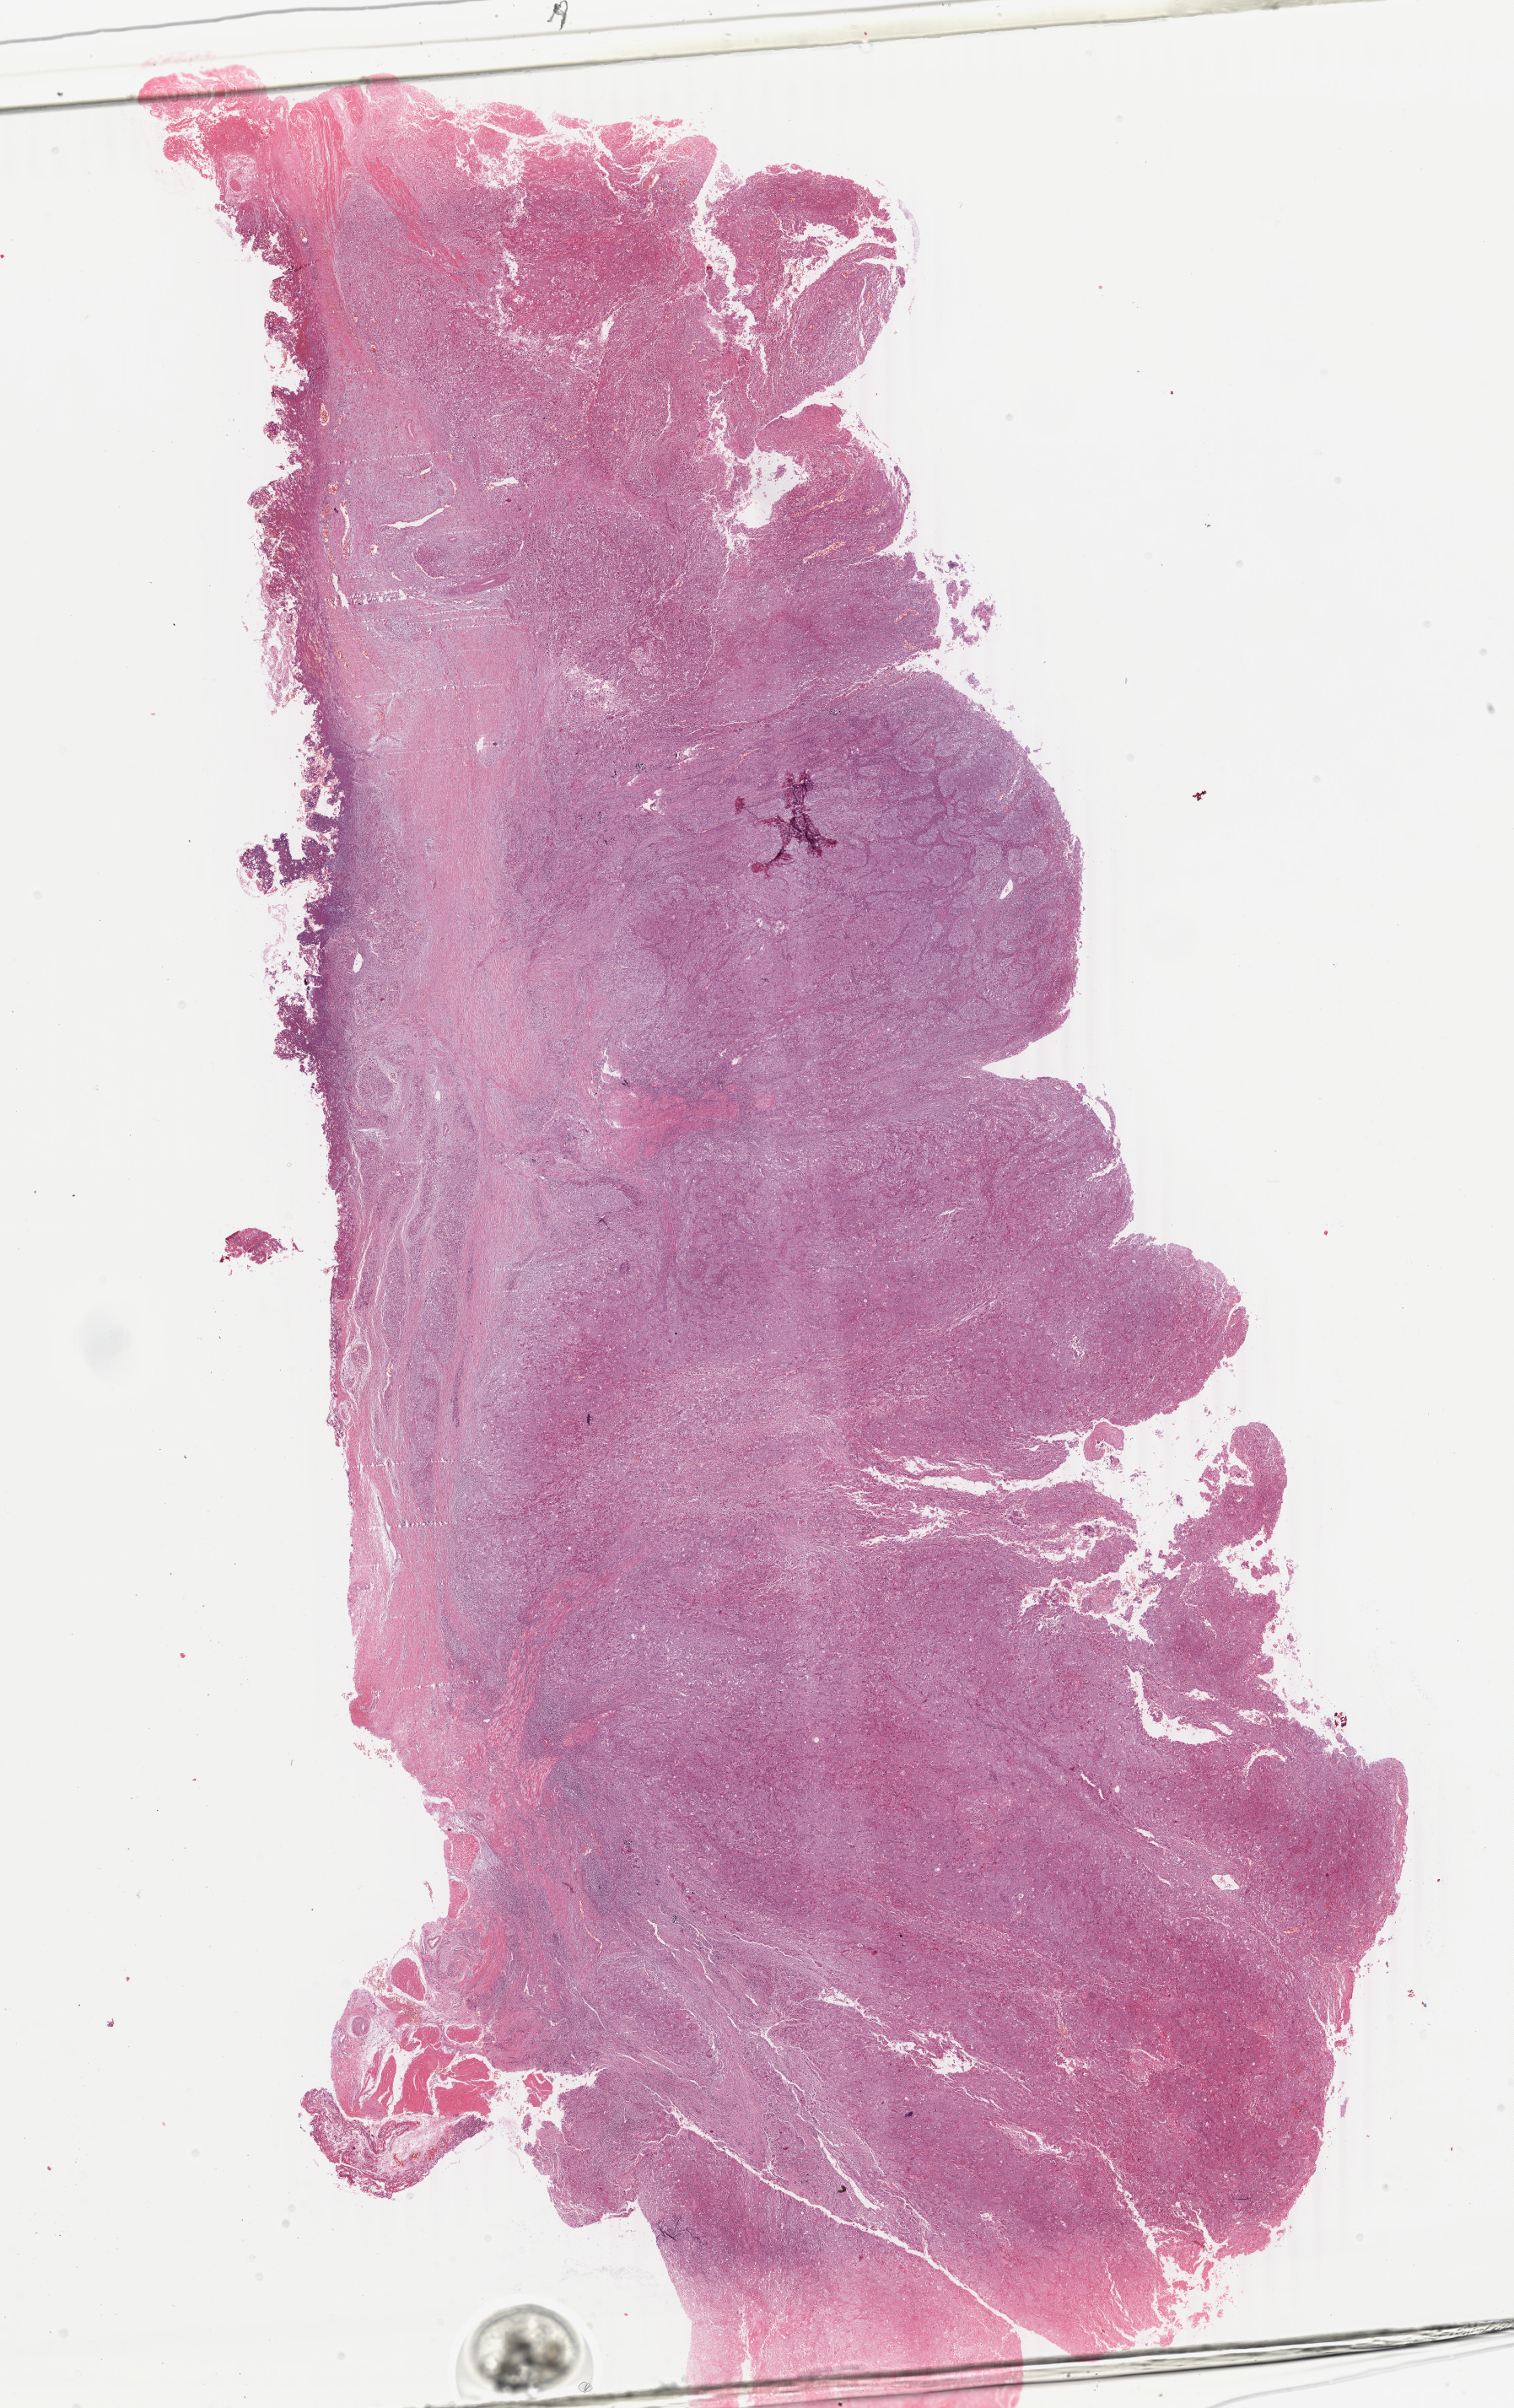
Hematoxylin and eosin (H&E) stained whole-slide image, whole scanned area (about 14.3 x 22.7 mm) shown as a low-resolution overview; formalin-fixed paraffin-embedded (FFPE) diagnostic section; primary tumour sample from the esophagus. Male, age 47 years at initial diagnosis. Histologic grade: G3 (poorly differentiated).
AJCC pathologic stage: IIA (6th edition). Histologic diagnosis: Squamous cell carcinoma, NOS (middle third of esophagus).